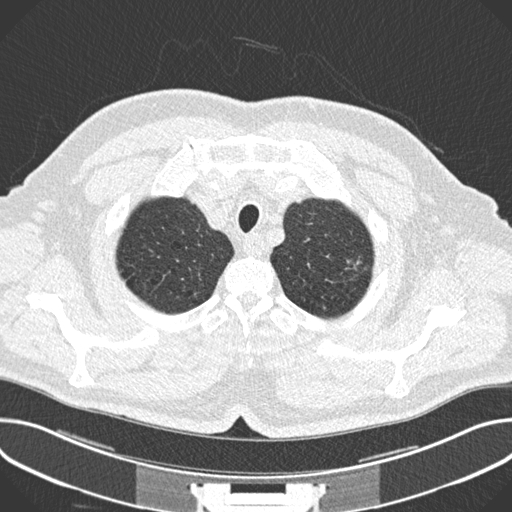
Axial slice from a low-dose chest CT screening exam. Baseline annual screen. Lung window (W 1500 / L -600 HU). Standard (soft-tissue) reconstruction kernel (B30f). Slice 29 of 245 in the series. Male participant, aged 63 years at enrolment. Current smoker at enrolment.
• Expert-annotated lung lesion, bounding box [x1, y1, x2, y2] px = [338, 250, 375, 282].
• The screening reader recorded 2 non-calcified nodules or masses ≥4 mm on this exam; which of them this box marks is not recorded.
• Participant outcome: lung cancer diagnosed 174 days after this screen — adenocarcinoma, NOS, left upper lobe, poorly differentiated (G3), stage IIIA (AJCC 6th edition), 11 mm at pathology.